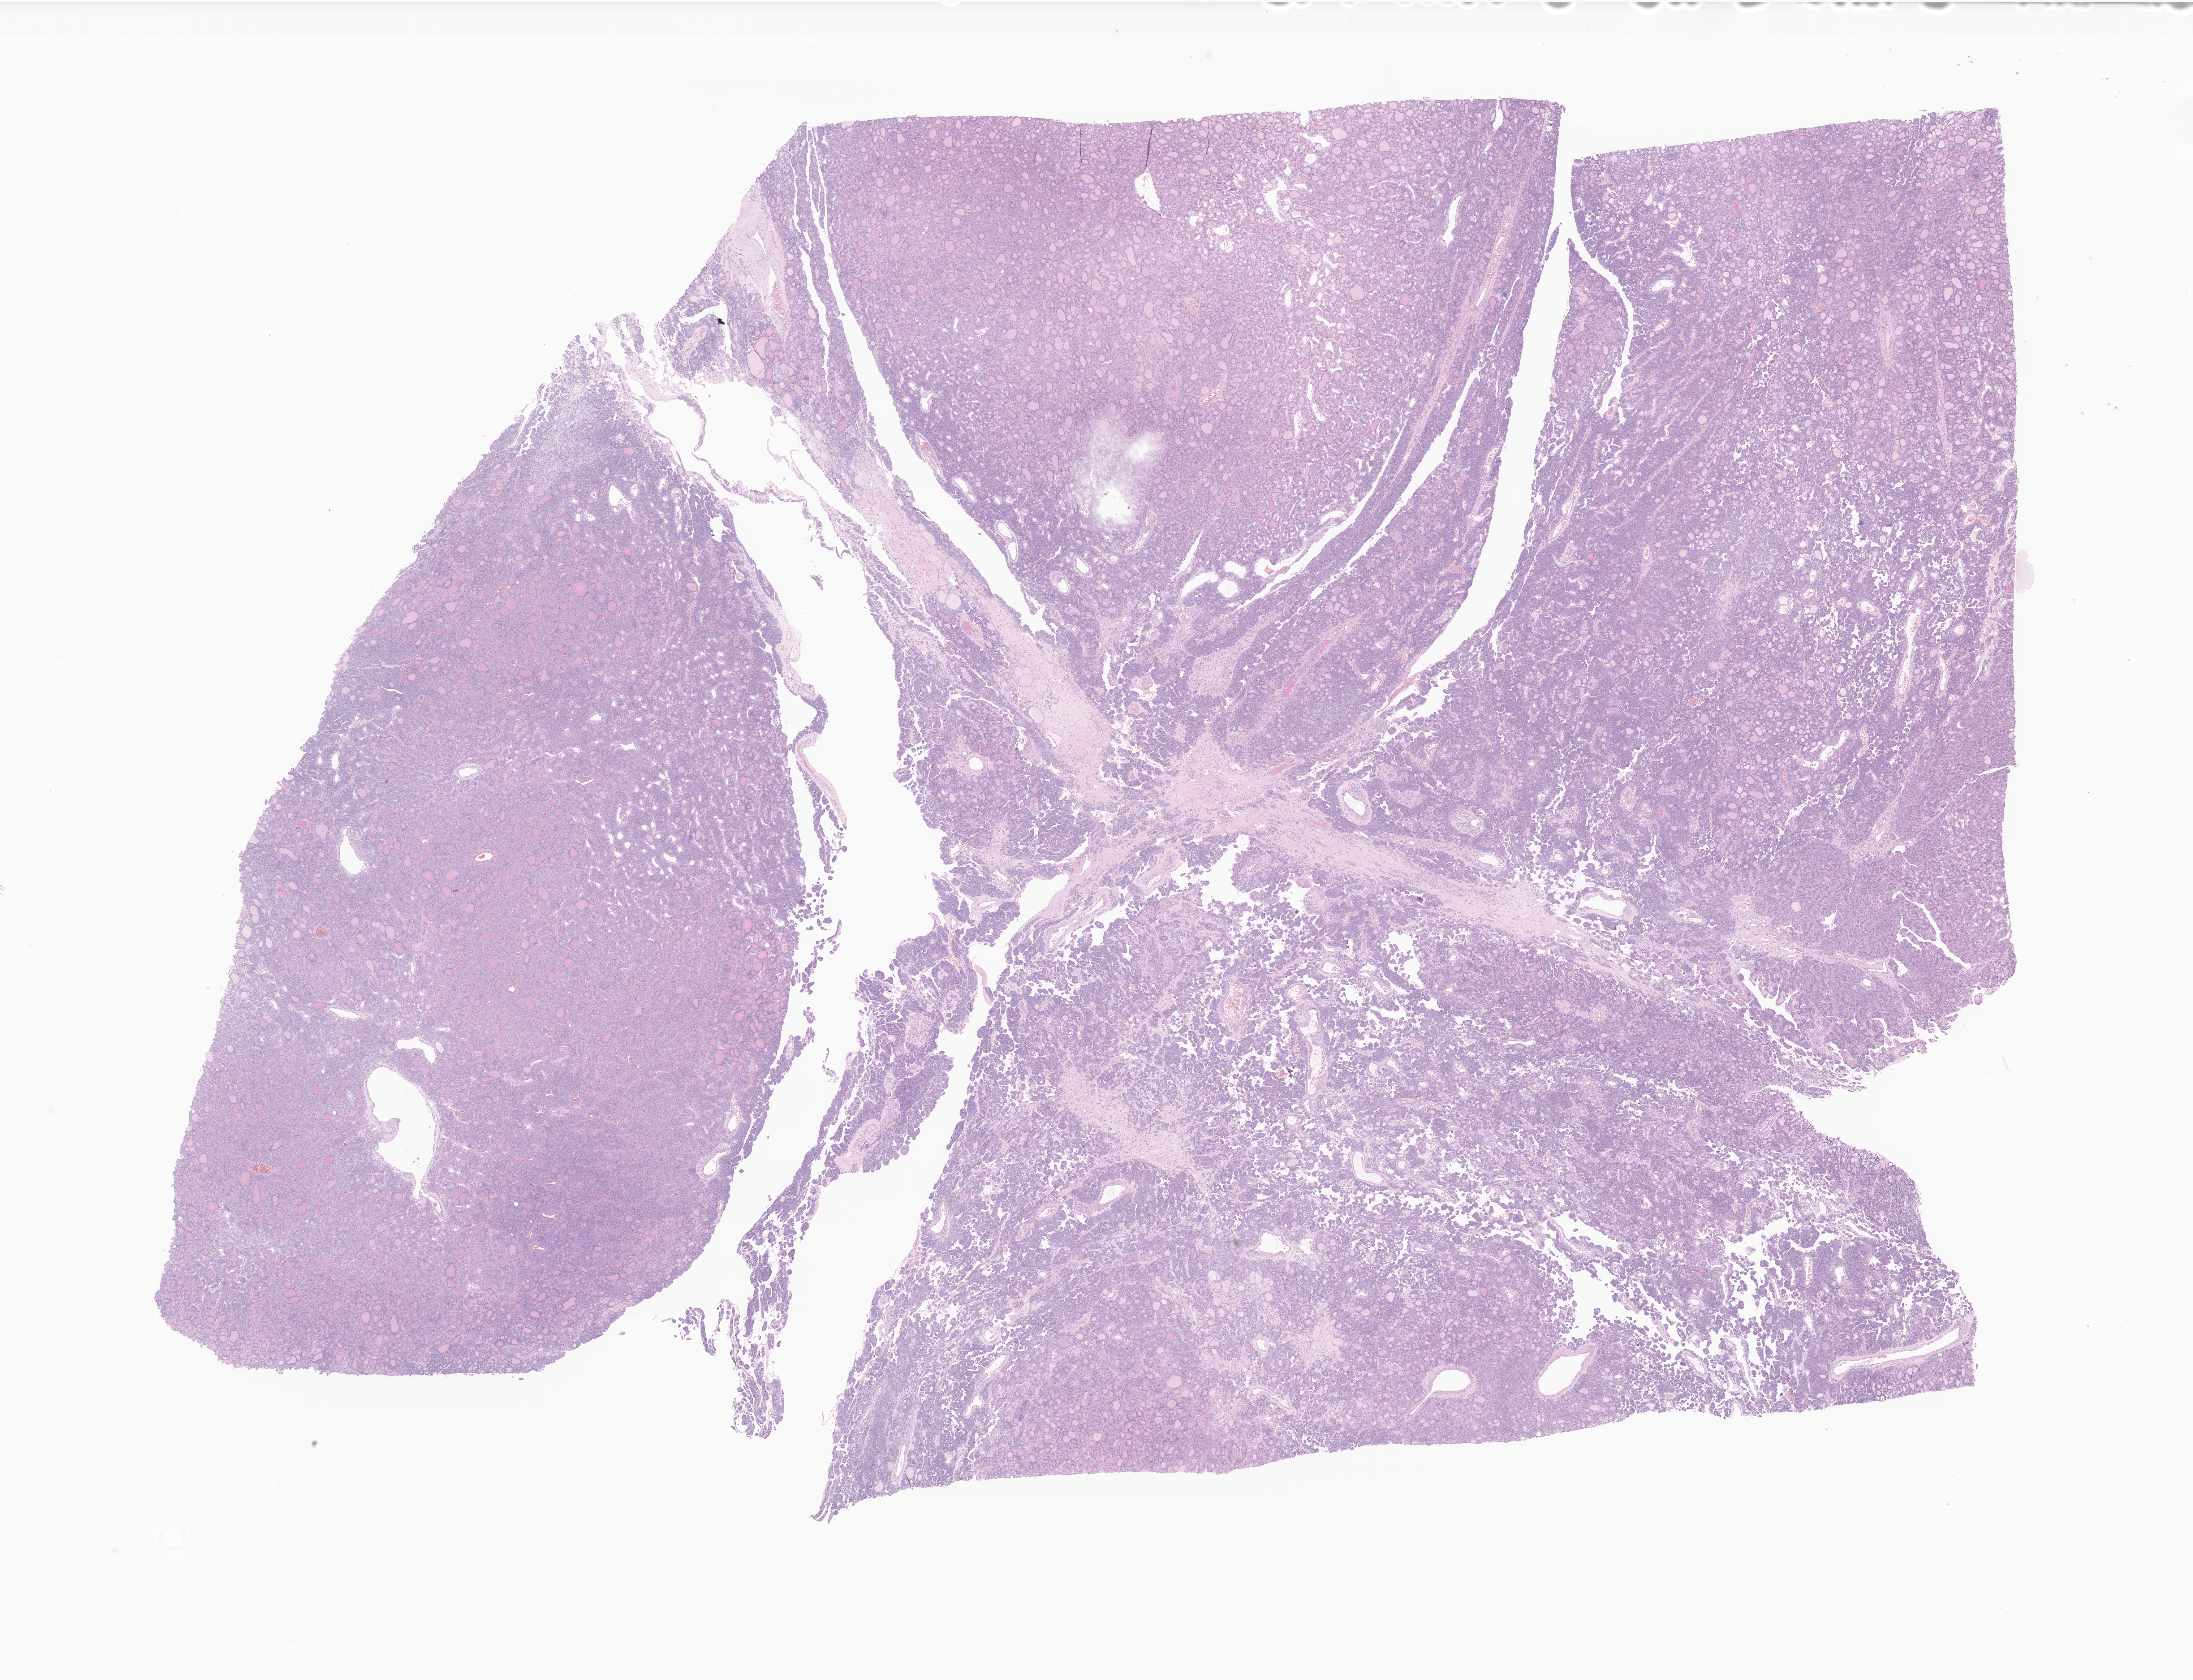
Hematoxylin and eosin (H&E) whole-slide image of tumor tissue from the thyroid — low-resolution overview of the scanned area, about 25.6 x 19.6 mm, formalin-fixed, paraffin-embedded (FFPE) tissue. Patient: female, age 176 months.
* recorded diagnosis: Follicular carcinoma, minimally invasive